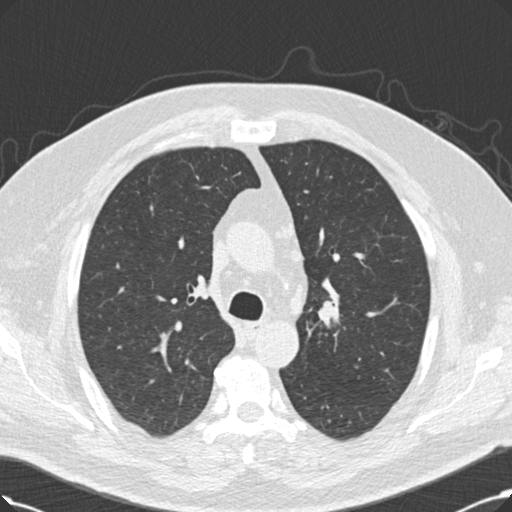
Low-dose screening chest CT, one axial slice; position 153 of 214 along the scan axis; reconstruction kernel B30f; 120 kVp; lung window (W 1500 / L -600 HU); 2 mm slice thickness; 512 × 512 image matrix.
Annotated regions visible in this slice (expert manual segmentation):
- lesion 1 (tumor): box from (x=318, y=300) to (x=339, y=327) px